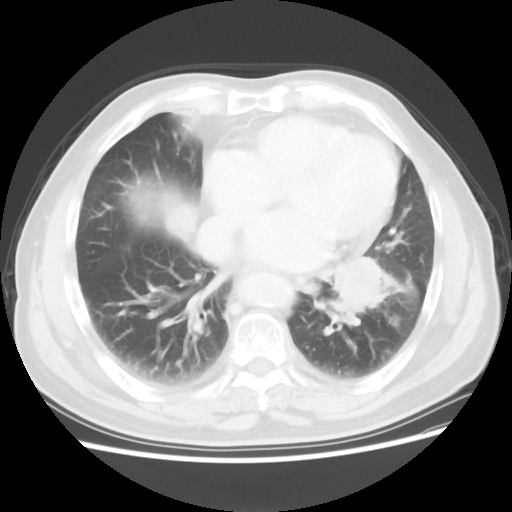
Chest CT, one axial slice; position 24 of 56 along the scan axis; reconstruction kernel STANDARD; lung window (W 1500 / L -600 HU); 5 mm slice thickness; 512 × 512 image matrix. Male patient, age 75 years. Case-level facts recorded for this patient, not image findings: clinical TNM (as recorded): T3 N0 M0.
Annotated regions visible in this slice (bounding box drawn by a radiologist):
- lung tumour (recorded histology: squamous cell carcinoma): box from (x=315, y=241) to (x=398, y=331) px